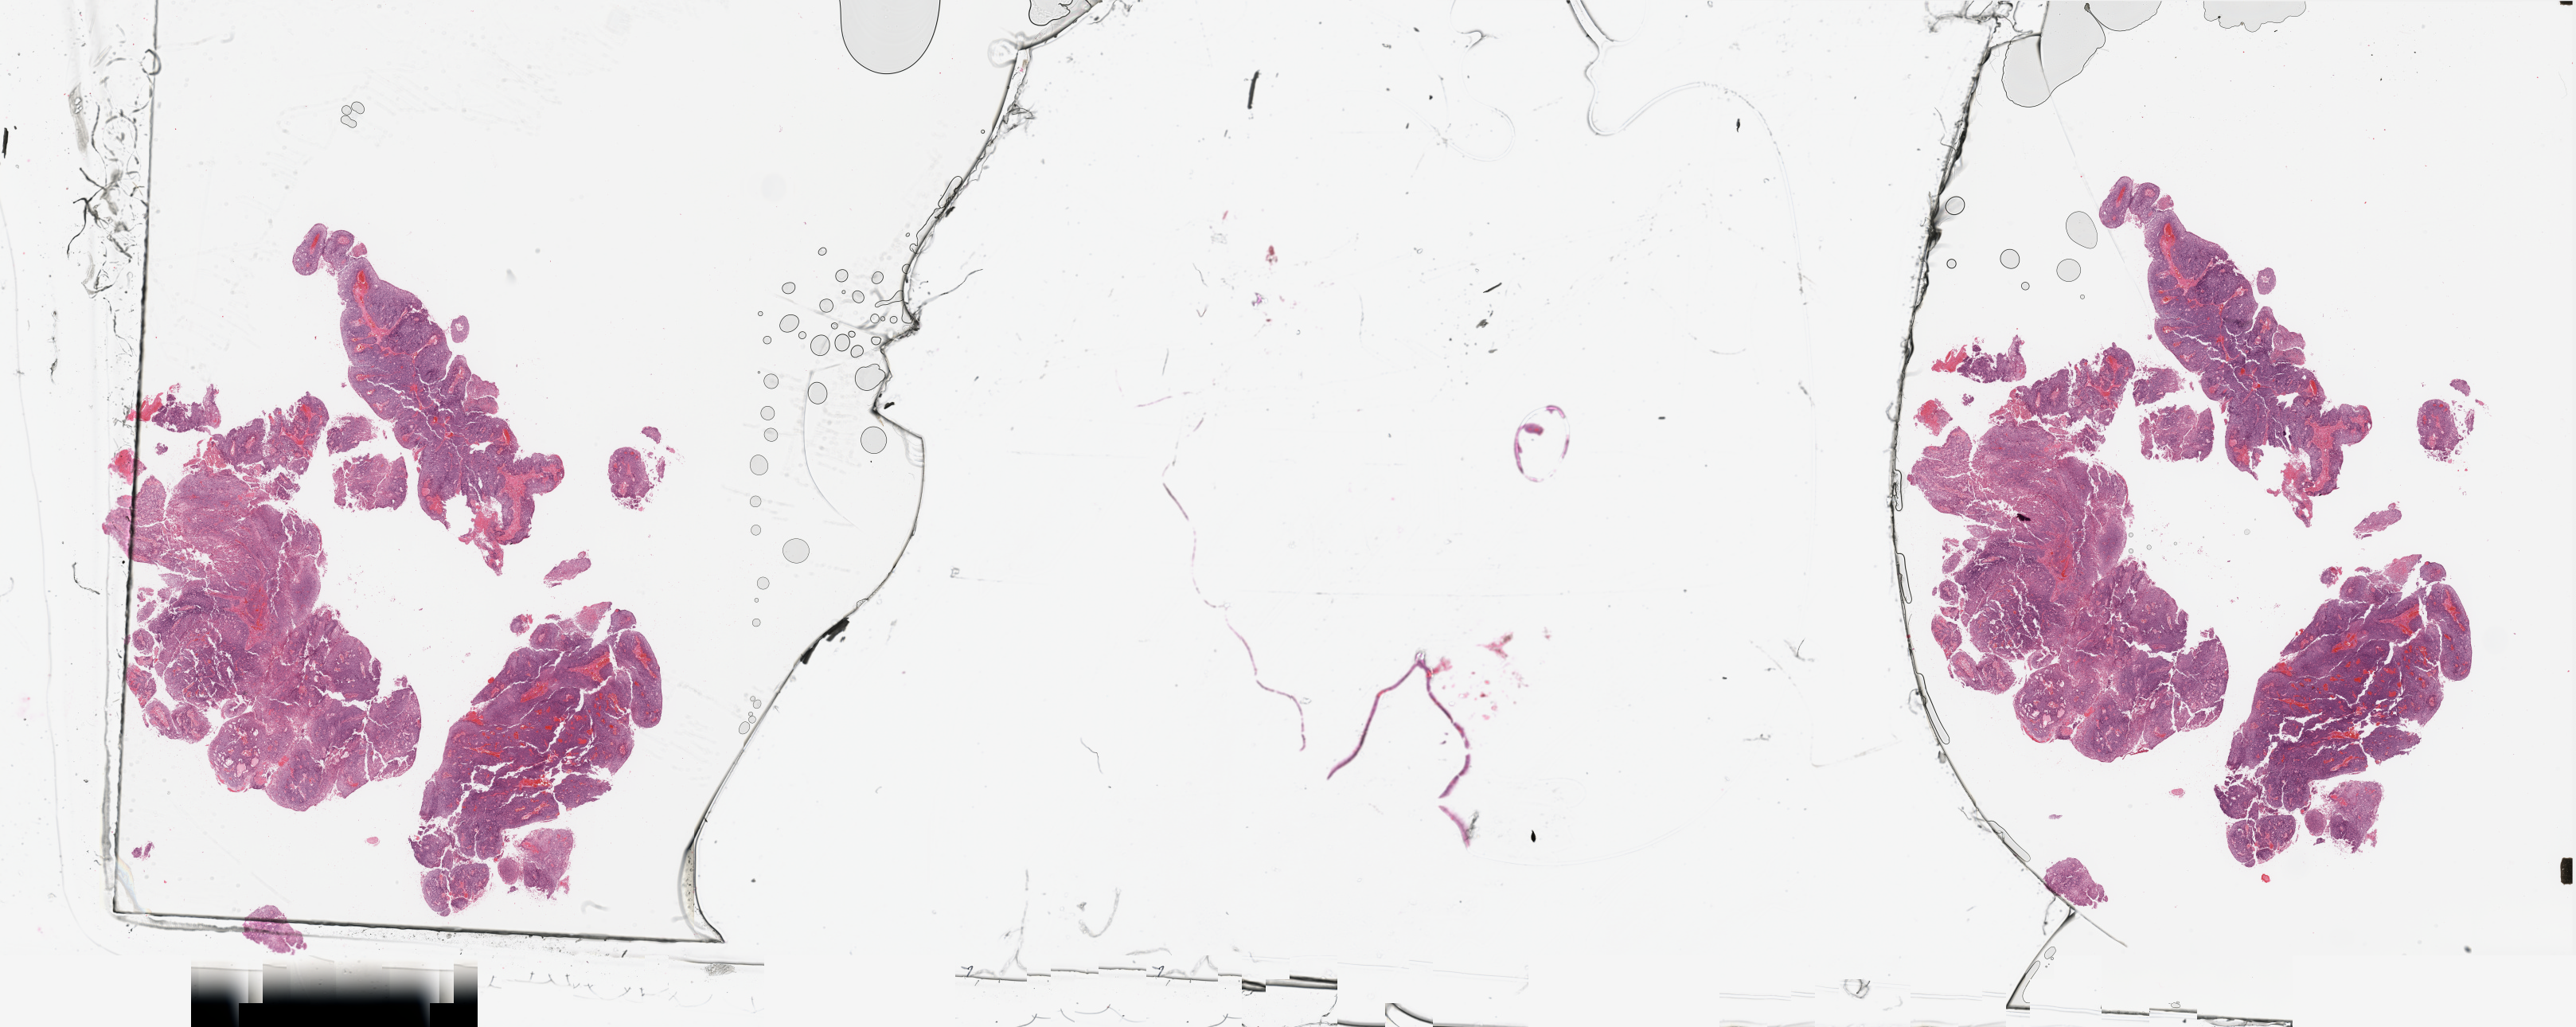
Whole-slide histology image, H&E-stained, low-resolution overview of the scanned area, about 51.2 x 20.4 mm (slide scanned at 20x); uterus, tumour tissue. Patient: female, age 53 years. Histologic grade: G2 (moderately differentiated).
- histologic diagnosis: Endometrioid adenocarcinoma, NOS
- AJCC pathologic stage: II